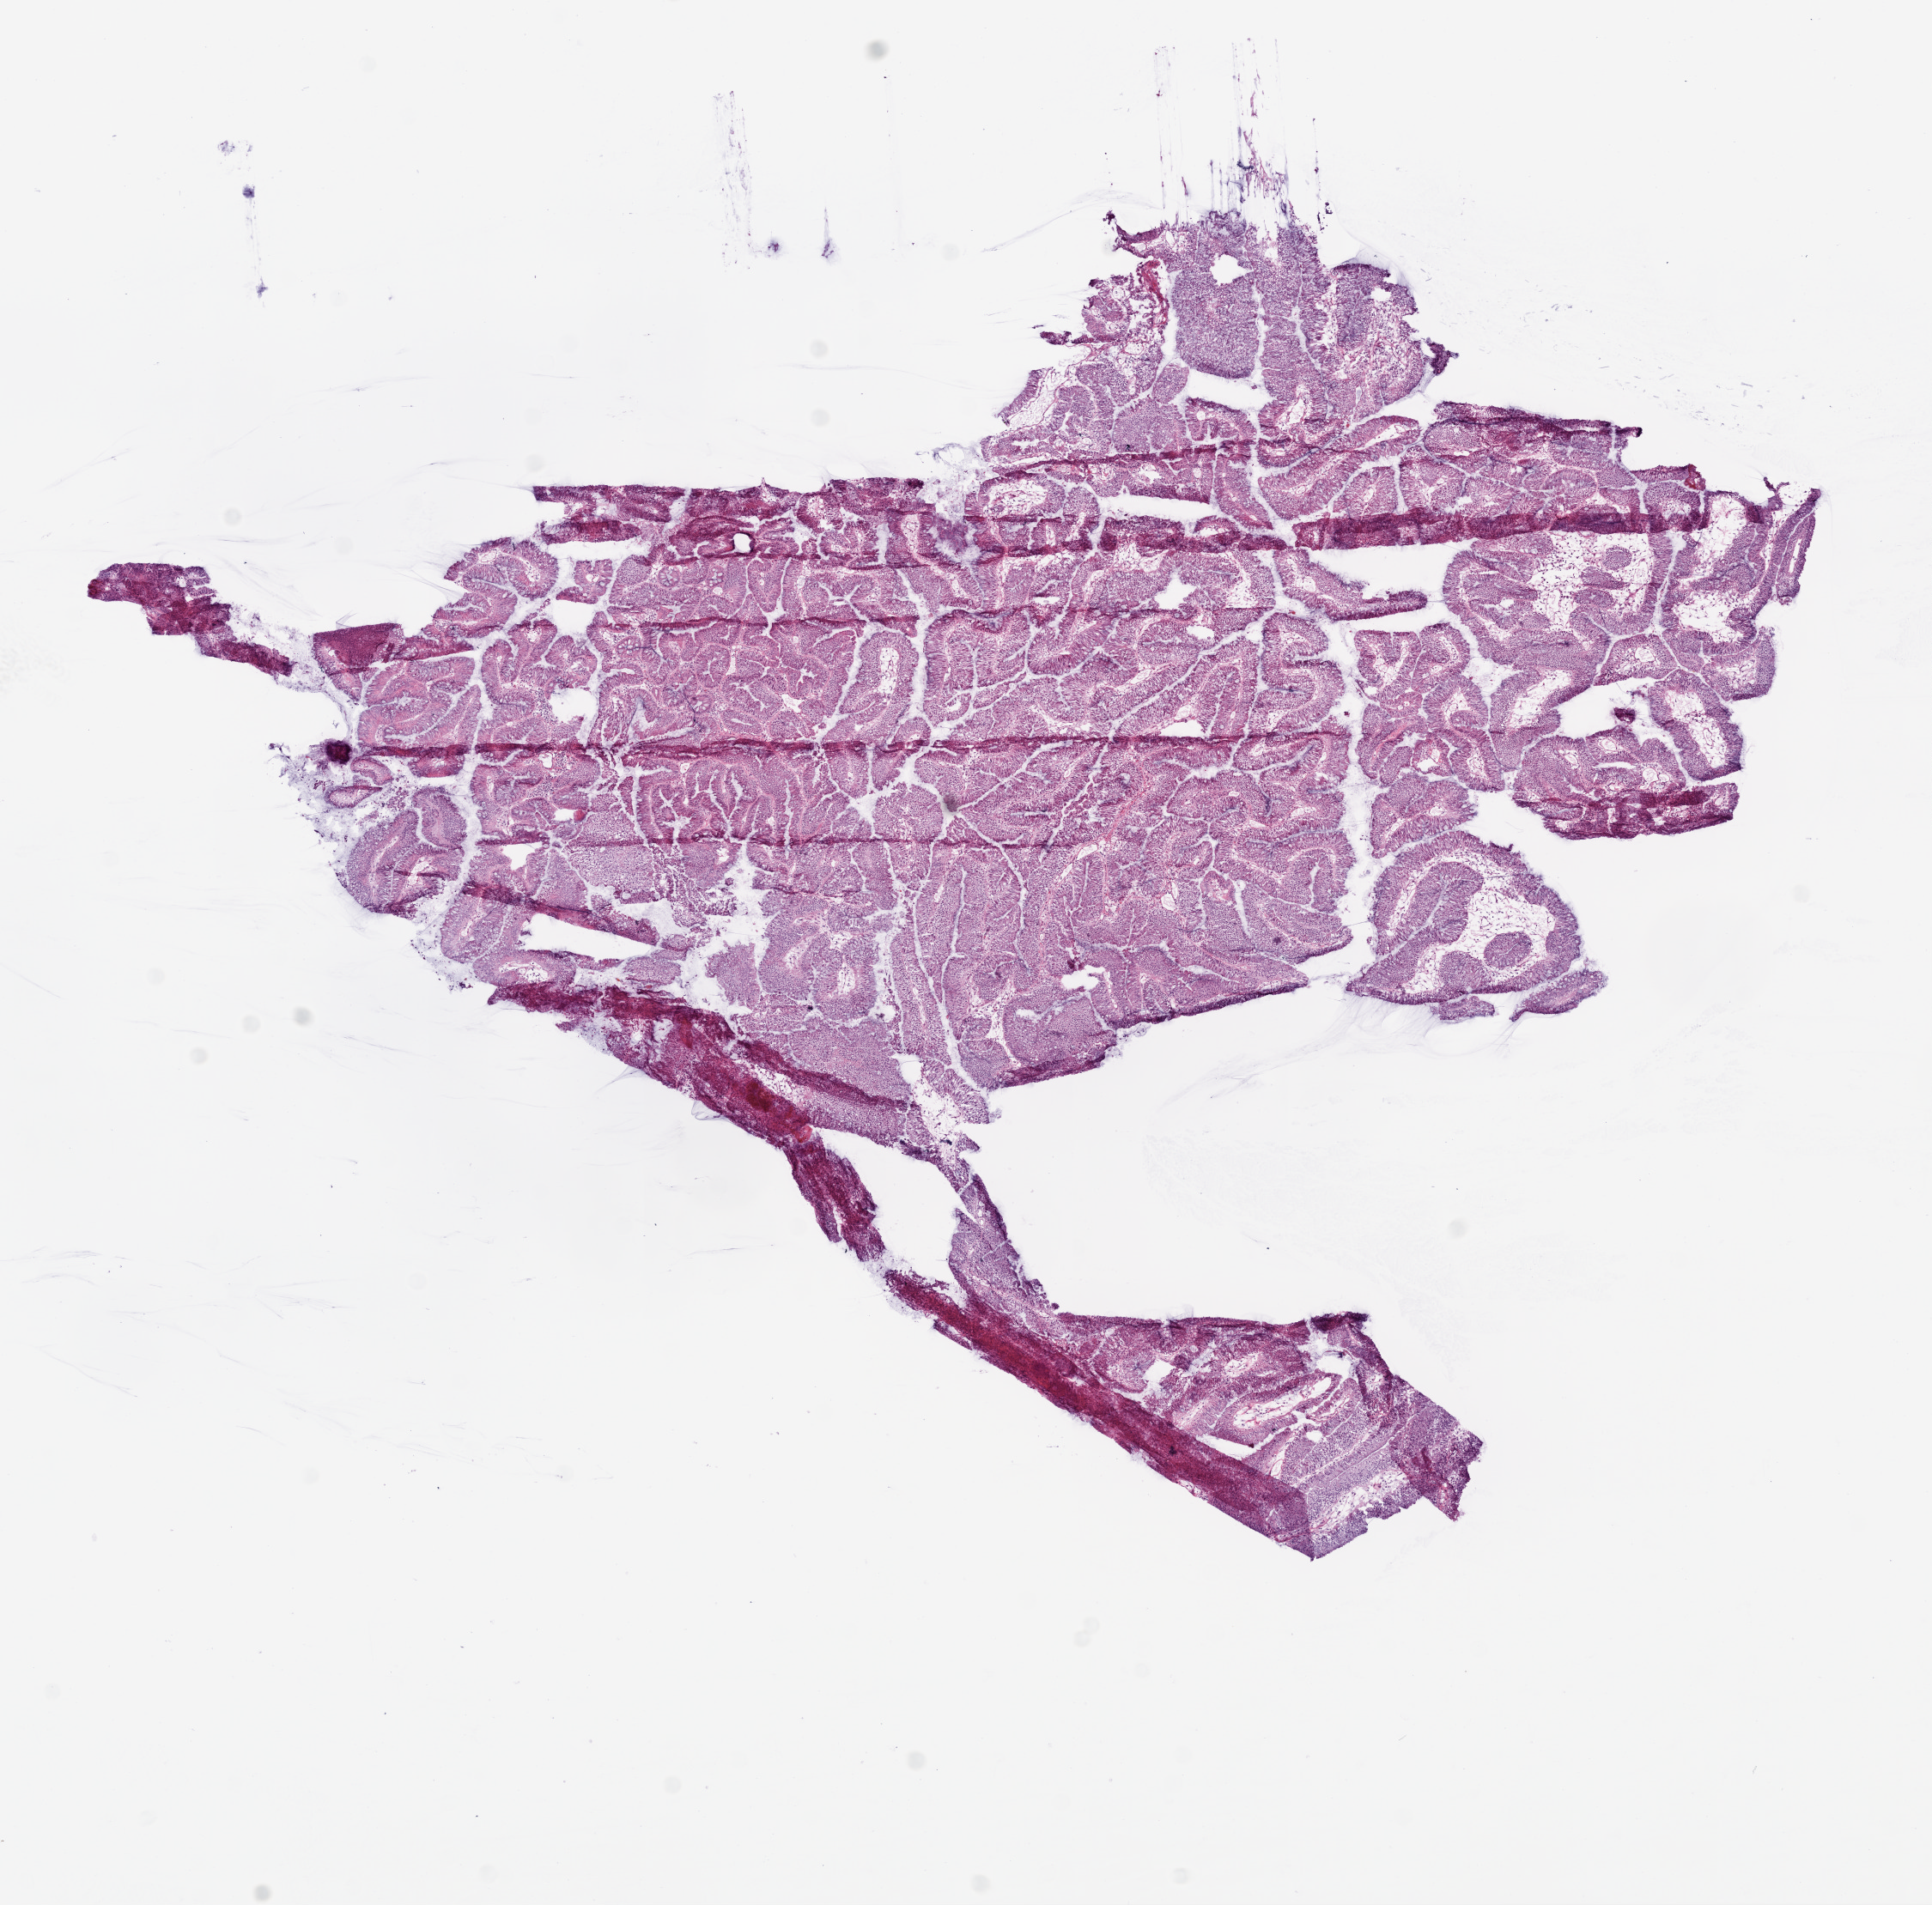
Whole-slide histology image, H&E-stained, shown as a low-resolution overview of the whole scanned area (about 9.0 x 8.9 mm, from a 20x scan), frozen section from the top of the tissue portion, sample: primary tumour, colon. Female, age 71 years at initial diagnosis. Slide review estimates, as recorded: tumour cells 95%, tumour nuclei 85%, normal cells 0%, stromal cells 5%, necrosis 0%.
Pathologic diagnosis: Mucinous adenocarcinoma. AJCC pathologic stage: I (6th edition).